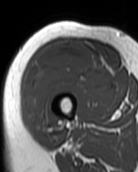
MRI of an extremity soft-tissue mass, one axial slice. Slice 36 of 99 in the series (ordered by position). MR volume resampled by the dataset authors to the PET/CT grid (not the native acquisition matrix). 3.27 mm slice thickness. 138 × 172 image matrix, field of view 135 × 168 mm. Female patient. Case-level facts recorded for this patient, not image findings: histological type: pleiomorphic undifferentiated sarcoma; grade: high; site of the primary tumour: right quadricep.
Annotated regions visible in this slice (expert contour drawn on MRI and transferred to this co-registered scan by the dataset authors):
- gross tumour volume including surrounding oedema: box from (x=25, y=43) to (x=109, y=129) px
- gross tumour volume (mass): (x=25, y=43)–(x=109, y=129)